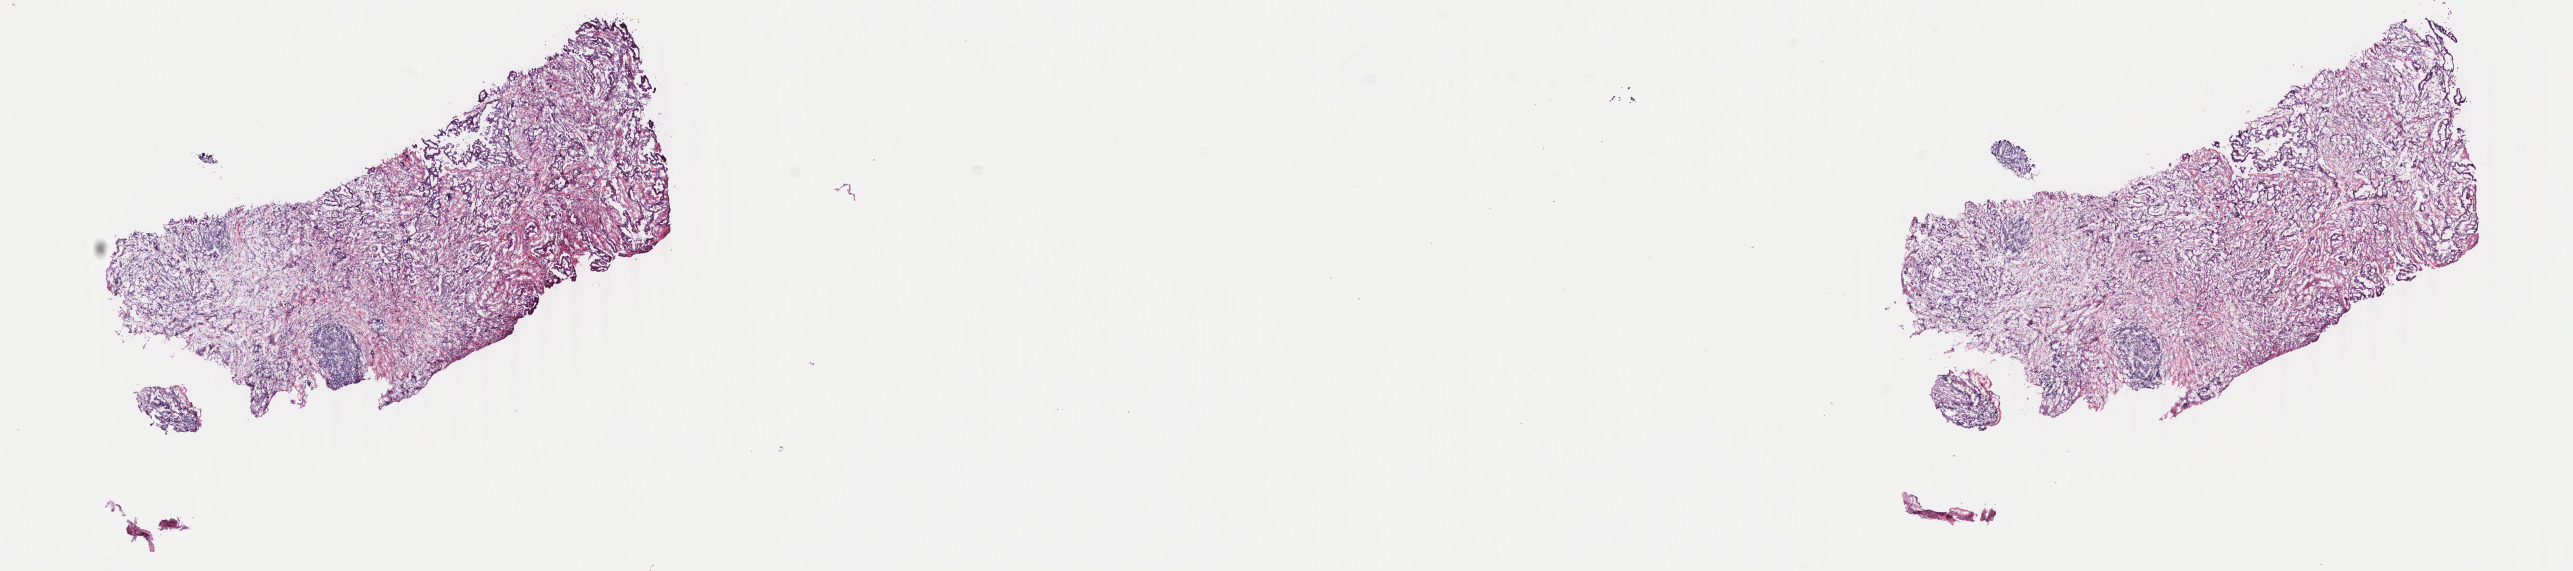
Whole-slide histology image, Hematoxylin and eosin (H&E) stained, low-resolution overview of the scanned area, about 20.5 x 4.5 mm (acquisition: 40x scan); frozen section; sample: primary tumour, pancreas. Male, age 70 years at initial diagnosis. Histologic grade: G2 (moderately differentiated). Slide review estimates, as recorded: tumour cells 27%, tumour nuclei 50%, normal cells 0%, stromal cells 71%, necrosis 2%. Inflammatory infiltration, as recorded: lymphocyte infiltration 35%, monocyte infiltration 3%, neutrophil infiltration 3%.
• histologic diagnosis: Infiltrating duct carcinoma, NOS (head of pancreas)
• AJCC pathologic stage: IIA (7th edition)